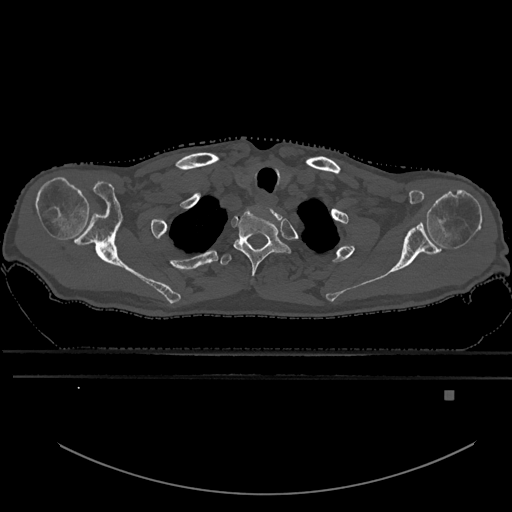
CT including the spine, one axial slice; position 534 of 969 along the scan axis; bone window (W 1800 / L 400 HU); 512 × 512 image matrix, field of view 456 × 456 mm. Patient: male, 82 years. Case-level facts recorded for this patient, not image findings: primary cancer: prostate.
Outlined on this slice (semi-automatically segmented with operator editing):
- T1 vertebra: bounding box (x1, y1, x2, y2) in pixels: (233, 210, 289, 277)
- T2 vertebra: (220, 254, 232, 266)